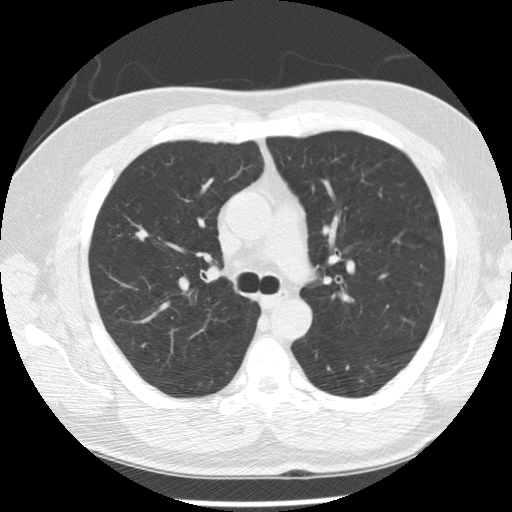
Low-dose screening chest CT, axial slice, first (baseline) screen, lung window (W 1500 / L -600 HU), 2.5 mm slice thickness, standard (soft-tissue) reconstruction kernel (STANDARD), 120 kVp, slice 90 of 265 in the series, 512 × 512 image matrix. Male participant, aged 57 years at enrolment. Former smoker at enrolment.
Expert reader's lesion annotation, bounding box [x1, y1, x2, y2] px = [124, 219, 158, 252]. The exam's reader record, not a measurement of the box and not confirmed to be the same lesion: non-calcified nodule or mass ≥4 mm, right upper lobe, 7 × 7 mm, poorly defined margins, soft tissue attenuation. Later outcome: lung cancer diagnosed 125 days after this screen — squamous cell carcinoma, NOS, right upper lobe, moderately differentiated (G2), stage IA (AJCC 6th edition), 10 mm at pathology.